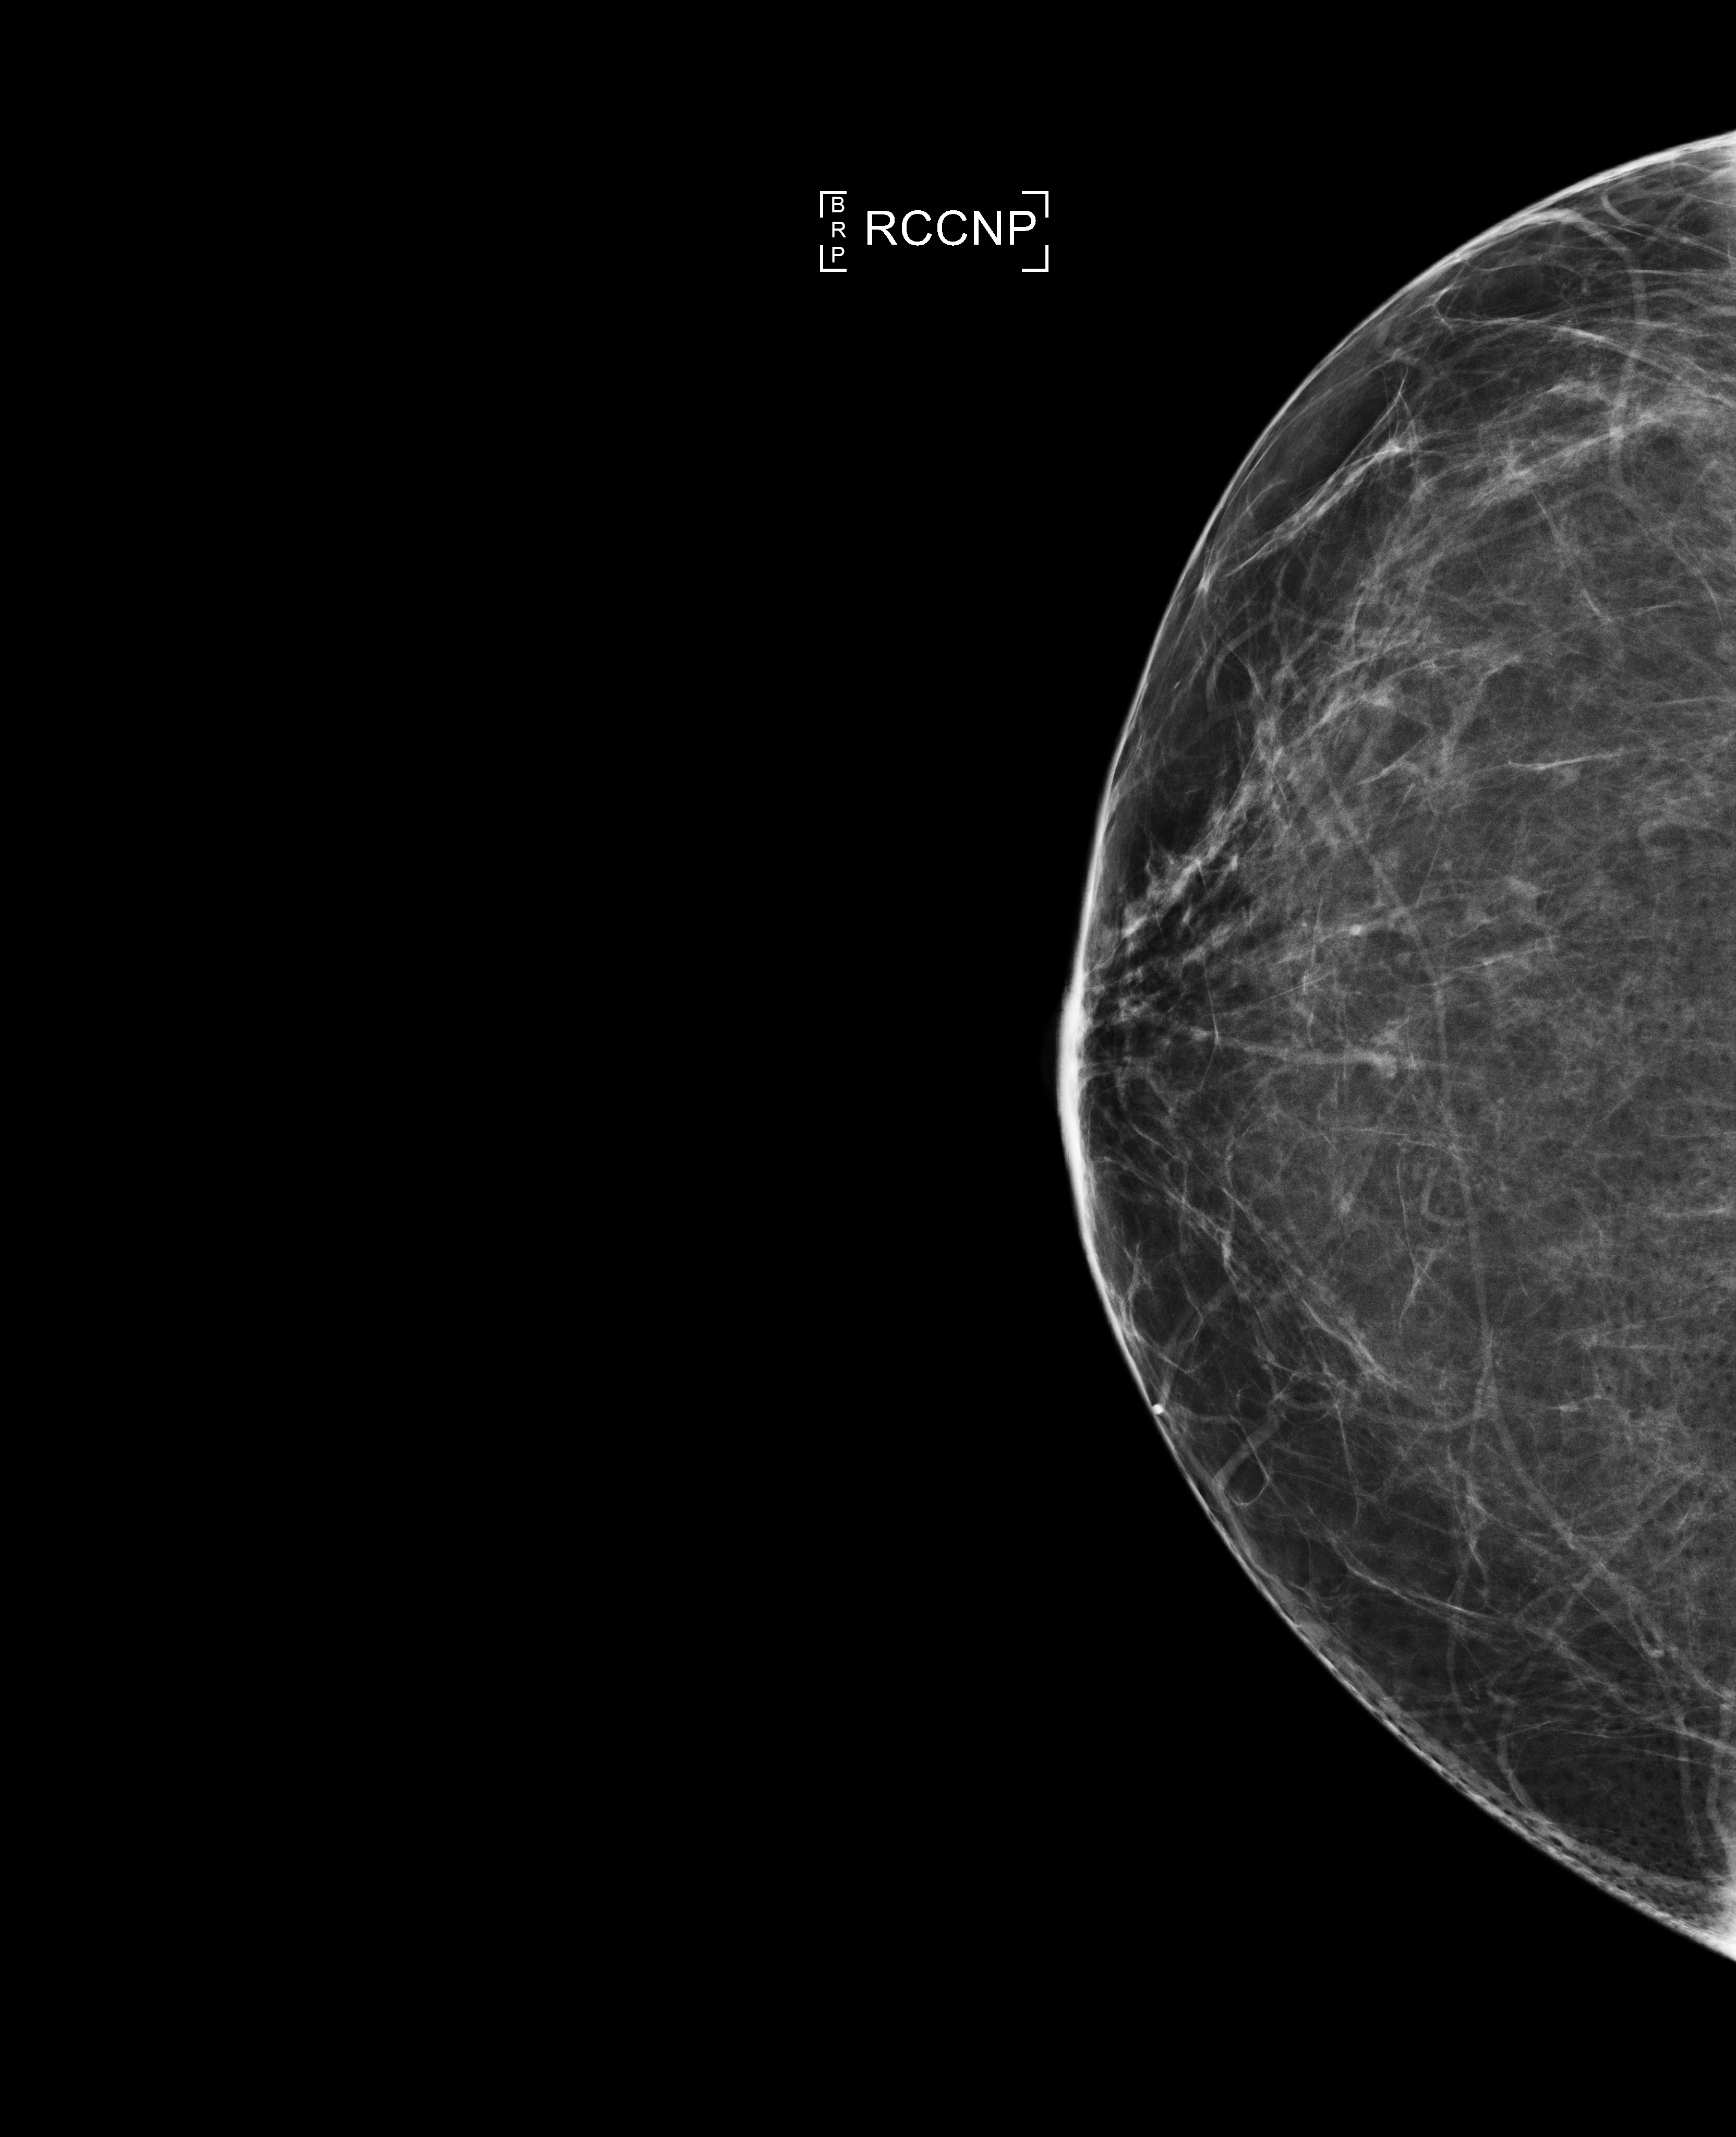
Screening examination, compressed breast thickness 72 mm, system: Selenia Dimensions. Female patient, age 51 years.
Image type: full-field digital mammogram. Breast: right. Projection: cranio-caudal projection, nipple in profile.